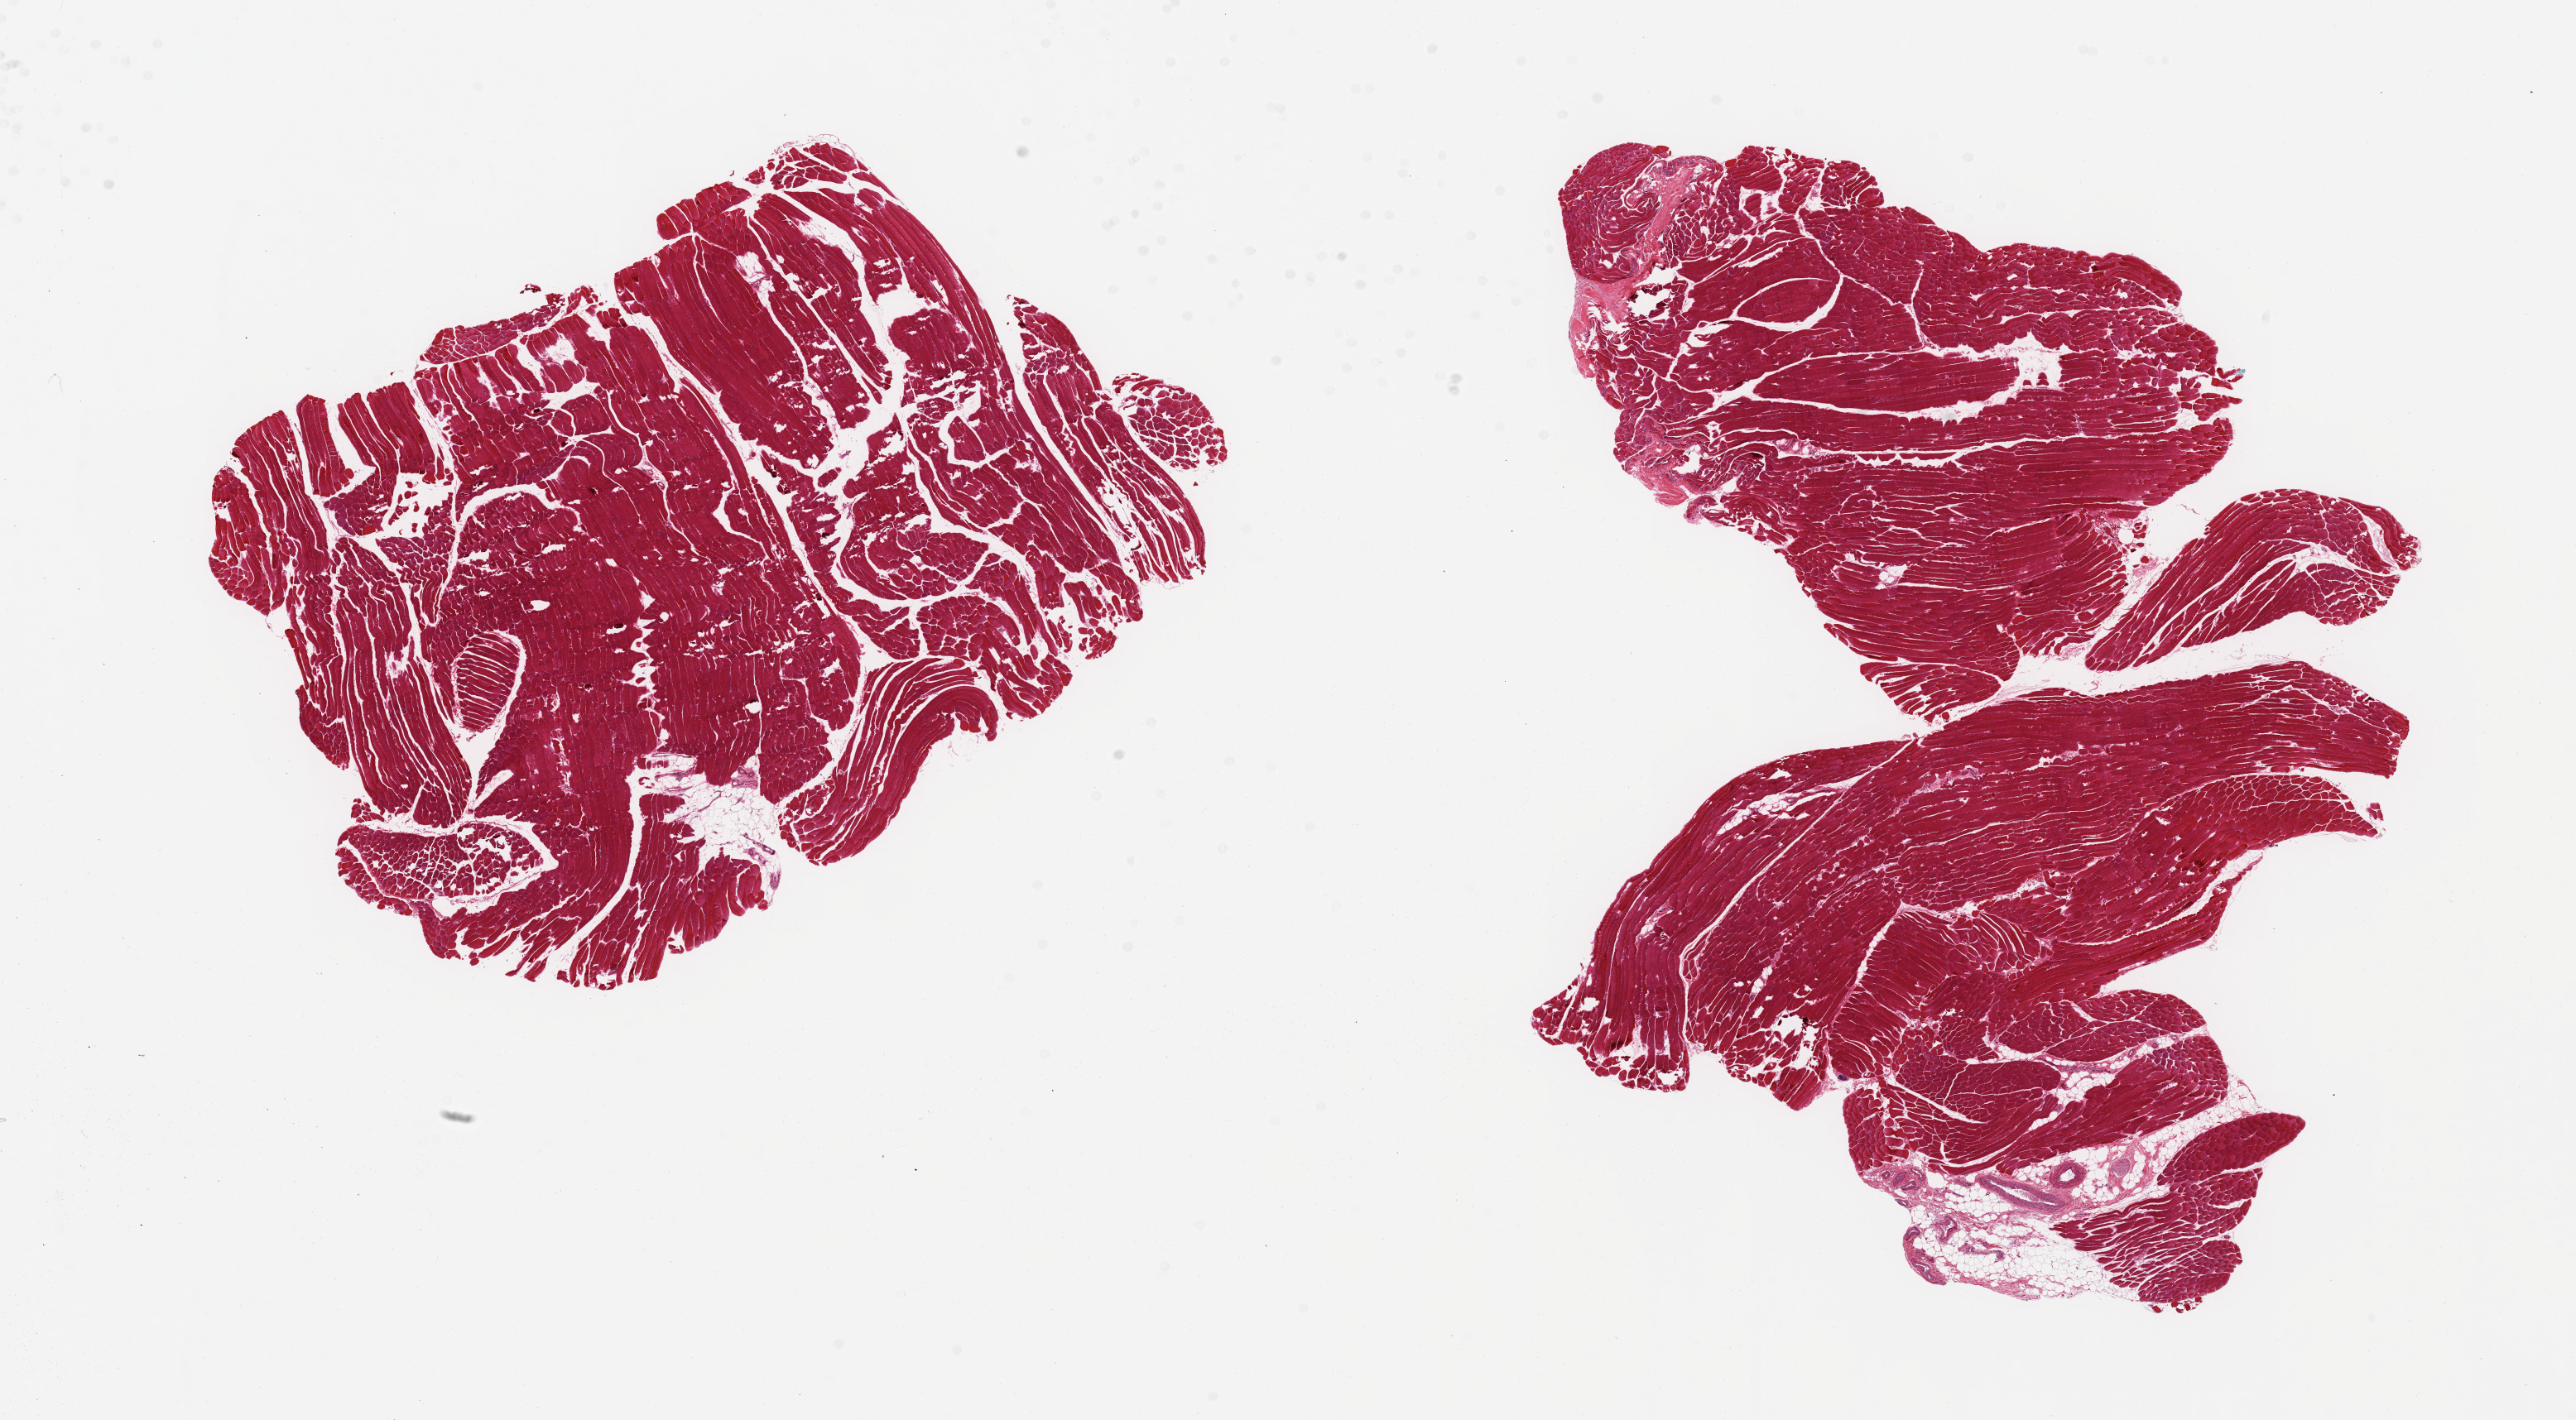
Whole-slide image, H&E stain, low-resolution overview of the scanned area, about 24.6 x 13.6 mm; PAXgene-fixed, paraffin-embedded tissue; target tissue: skeletal muscle; donor tissue sample. Male donor.
Pathologist's review note for this sample: 3 pieces, ~7x7mm pieces areas of underfixation.